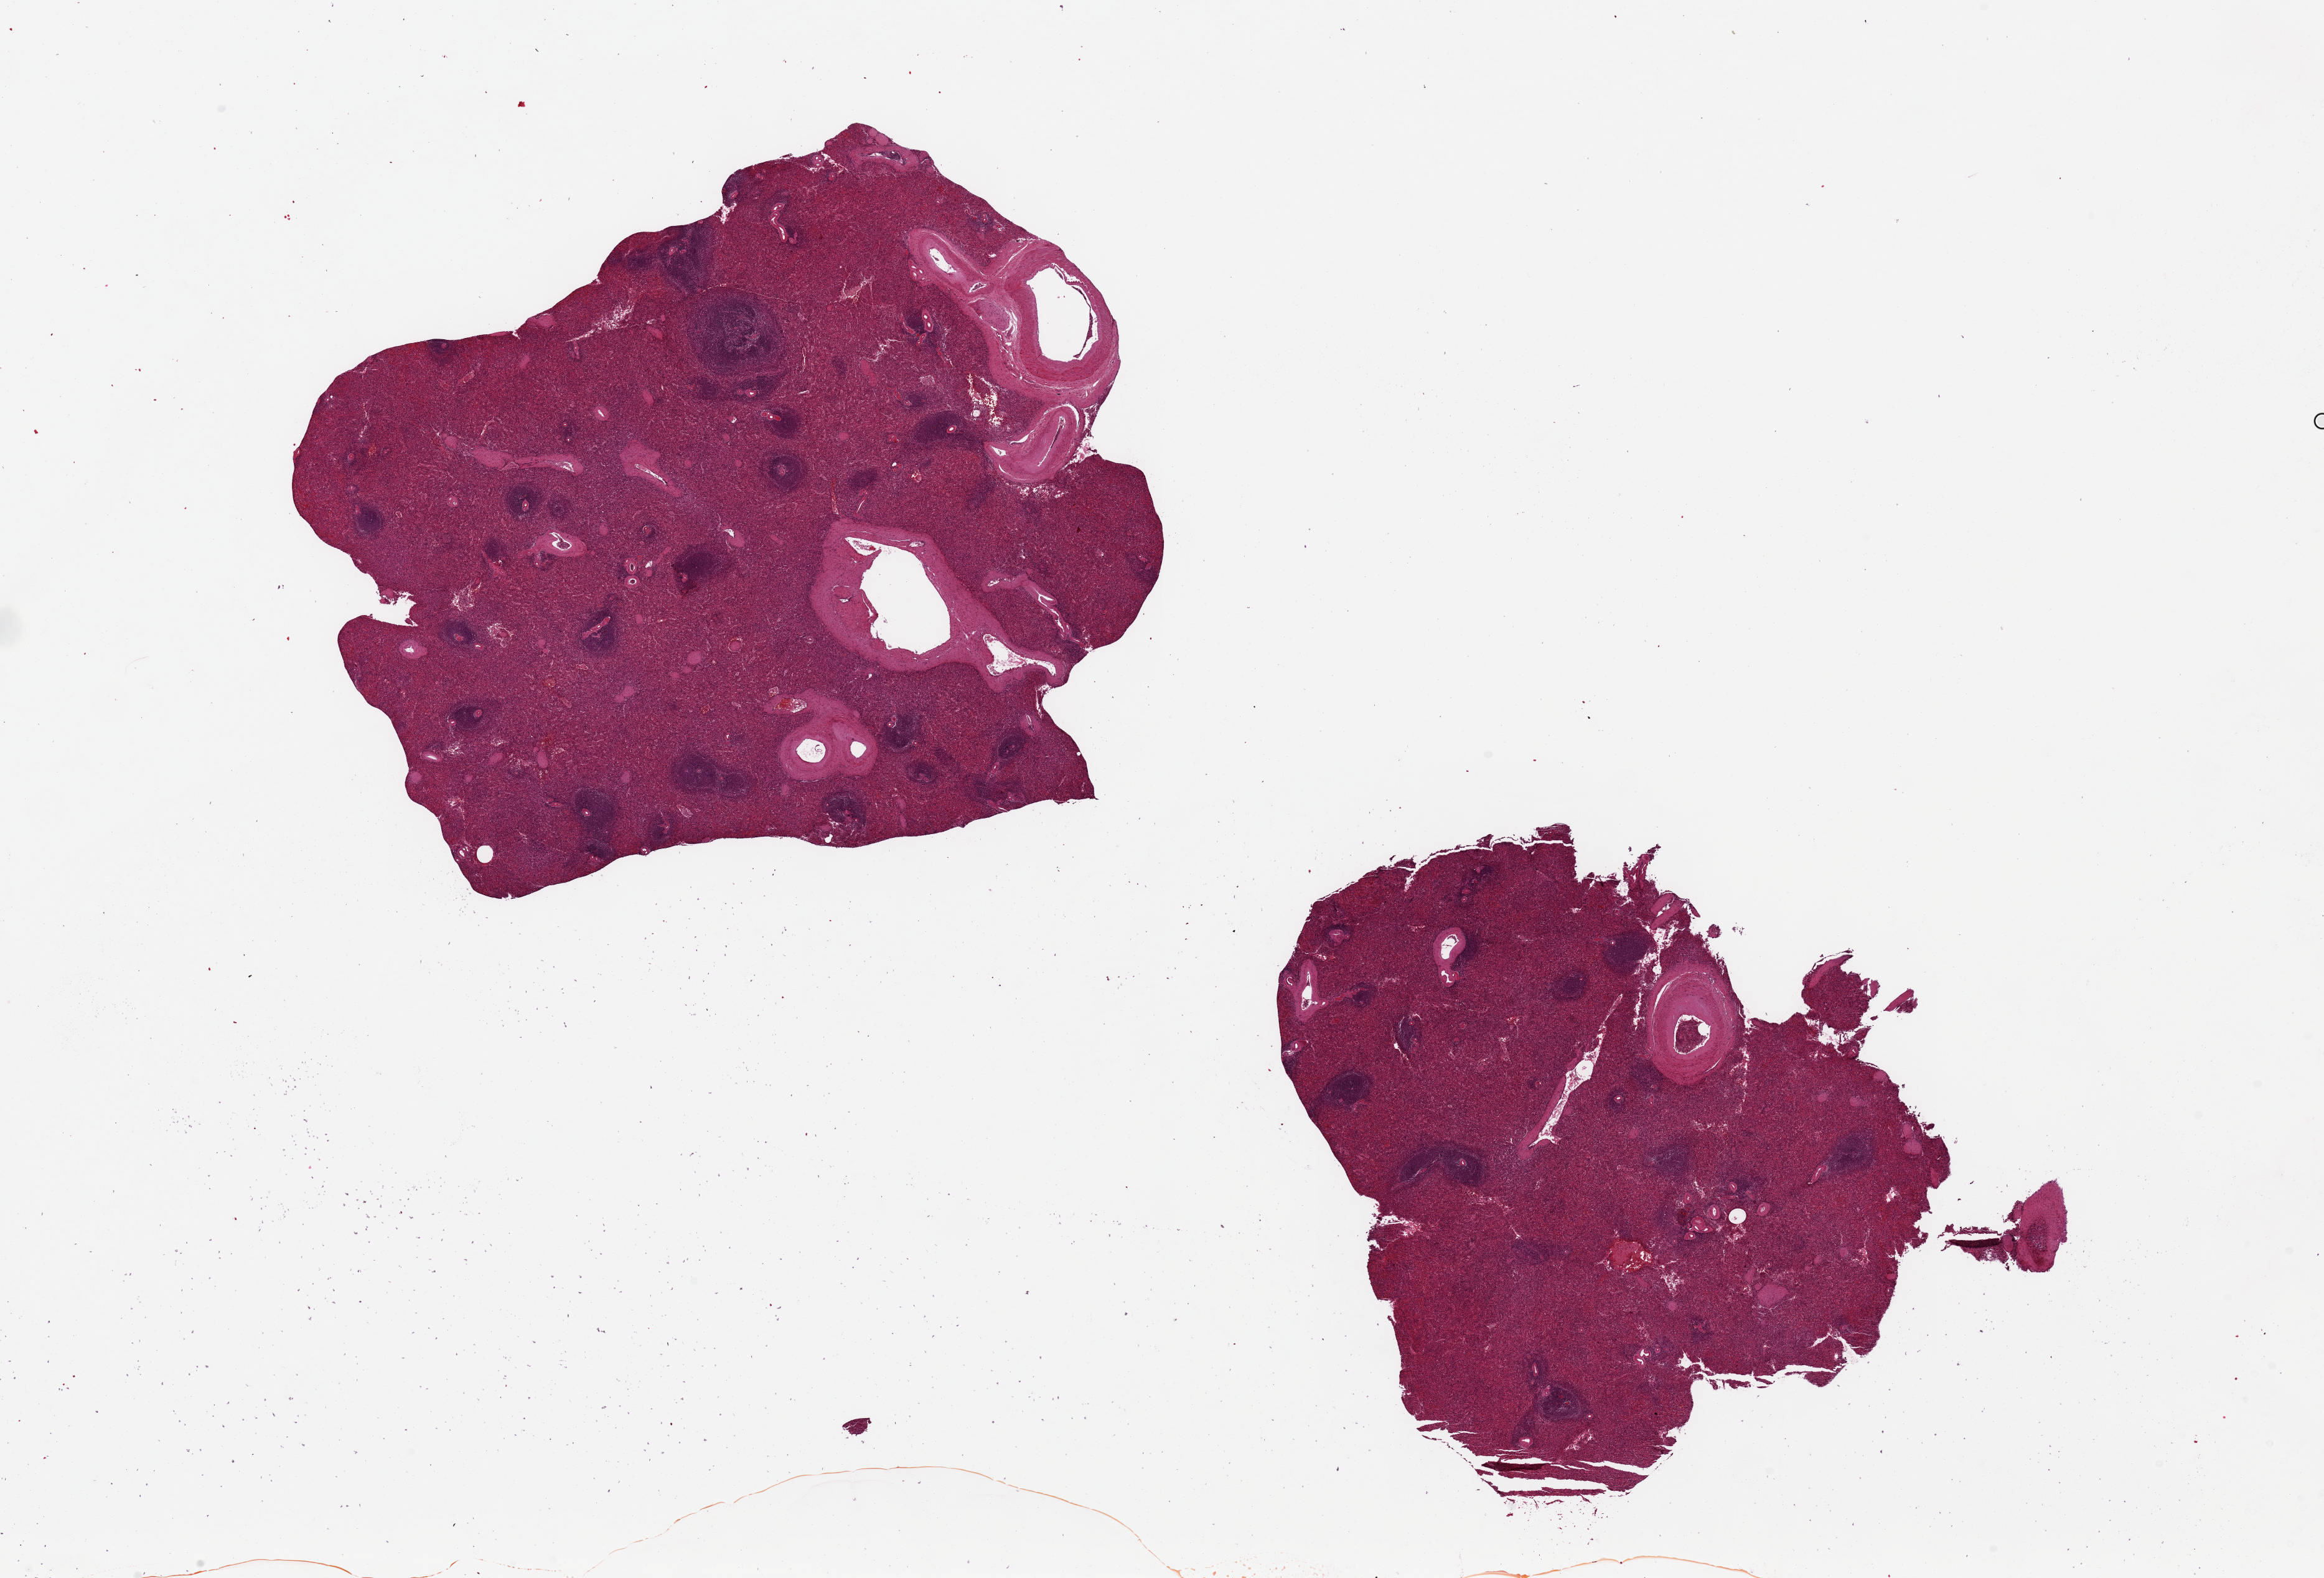
Haematoxylin and eosin whole-slide image — shown as a low-resolution overview of the whole scanned area (about 29.5 x 20.0 mm), PAXgene-fixed paraffin-embedded (PFPE) section, sampled site (target tissue): spleen, donor tissue sample.
* review note (as recorded): 2 pieces ~10x8mm